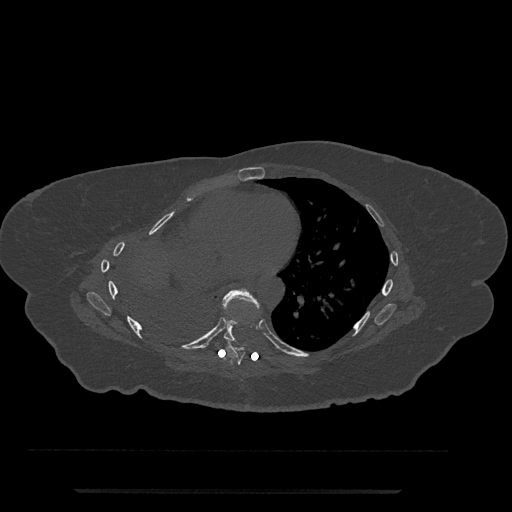
CT including the spine, one axial slice; position 418 of 797 along the scan axis; reconstruction kernel Br40s/3; 120 kVp; bone window (W 1800 / L 400 HU); 0.5 mm slice thickness; 512 × 512 image matrix. Patient: female, 51 years. Case-level facts recorded for this patient, not image findings: primary cancer: neuro; vertebrae with lytic lesions (as recorded): T8.
Annotated regions visible in this slice (semi-automatically segmented with operator editing):
- T7 vertebra: bounding box [x1, y1, x2, y2] px = [224, 341, 245, 365]
- T8 vertebra: [223, 288, 260, 342]